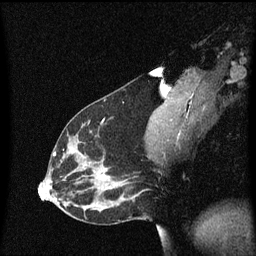
Breast MRI (dynamic contrast-enhanced), one sagittal slice; position 31 of 60 along the scan axis; dynamic contrast-enhanced series, image 2 of 3 at this slice position (ordered by acquisition); 1.5 T; TE 4.2 ms, TR 8.4 ms; 2 mm slice thickness; 256 × 256 image matrix. Female patient, age 33 years.
Annotated regions visible in this slice (semi-automatically segmented with operator editing):
- analysis volume of interest (the breast-tissue region the enhancement analysis was run in; not a lesion): bounding box [x1, y1, x2, y2] px = [45, 114, 152, 191]
- tumour enhancement mask (voxels above the 70 % enhancement threshold inside the analysis volume of interest): [54, 120, 111, 179]